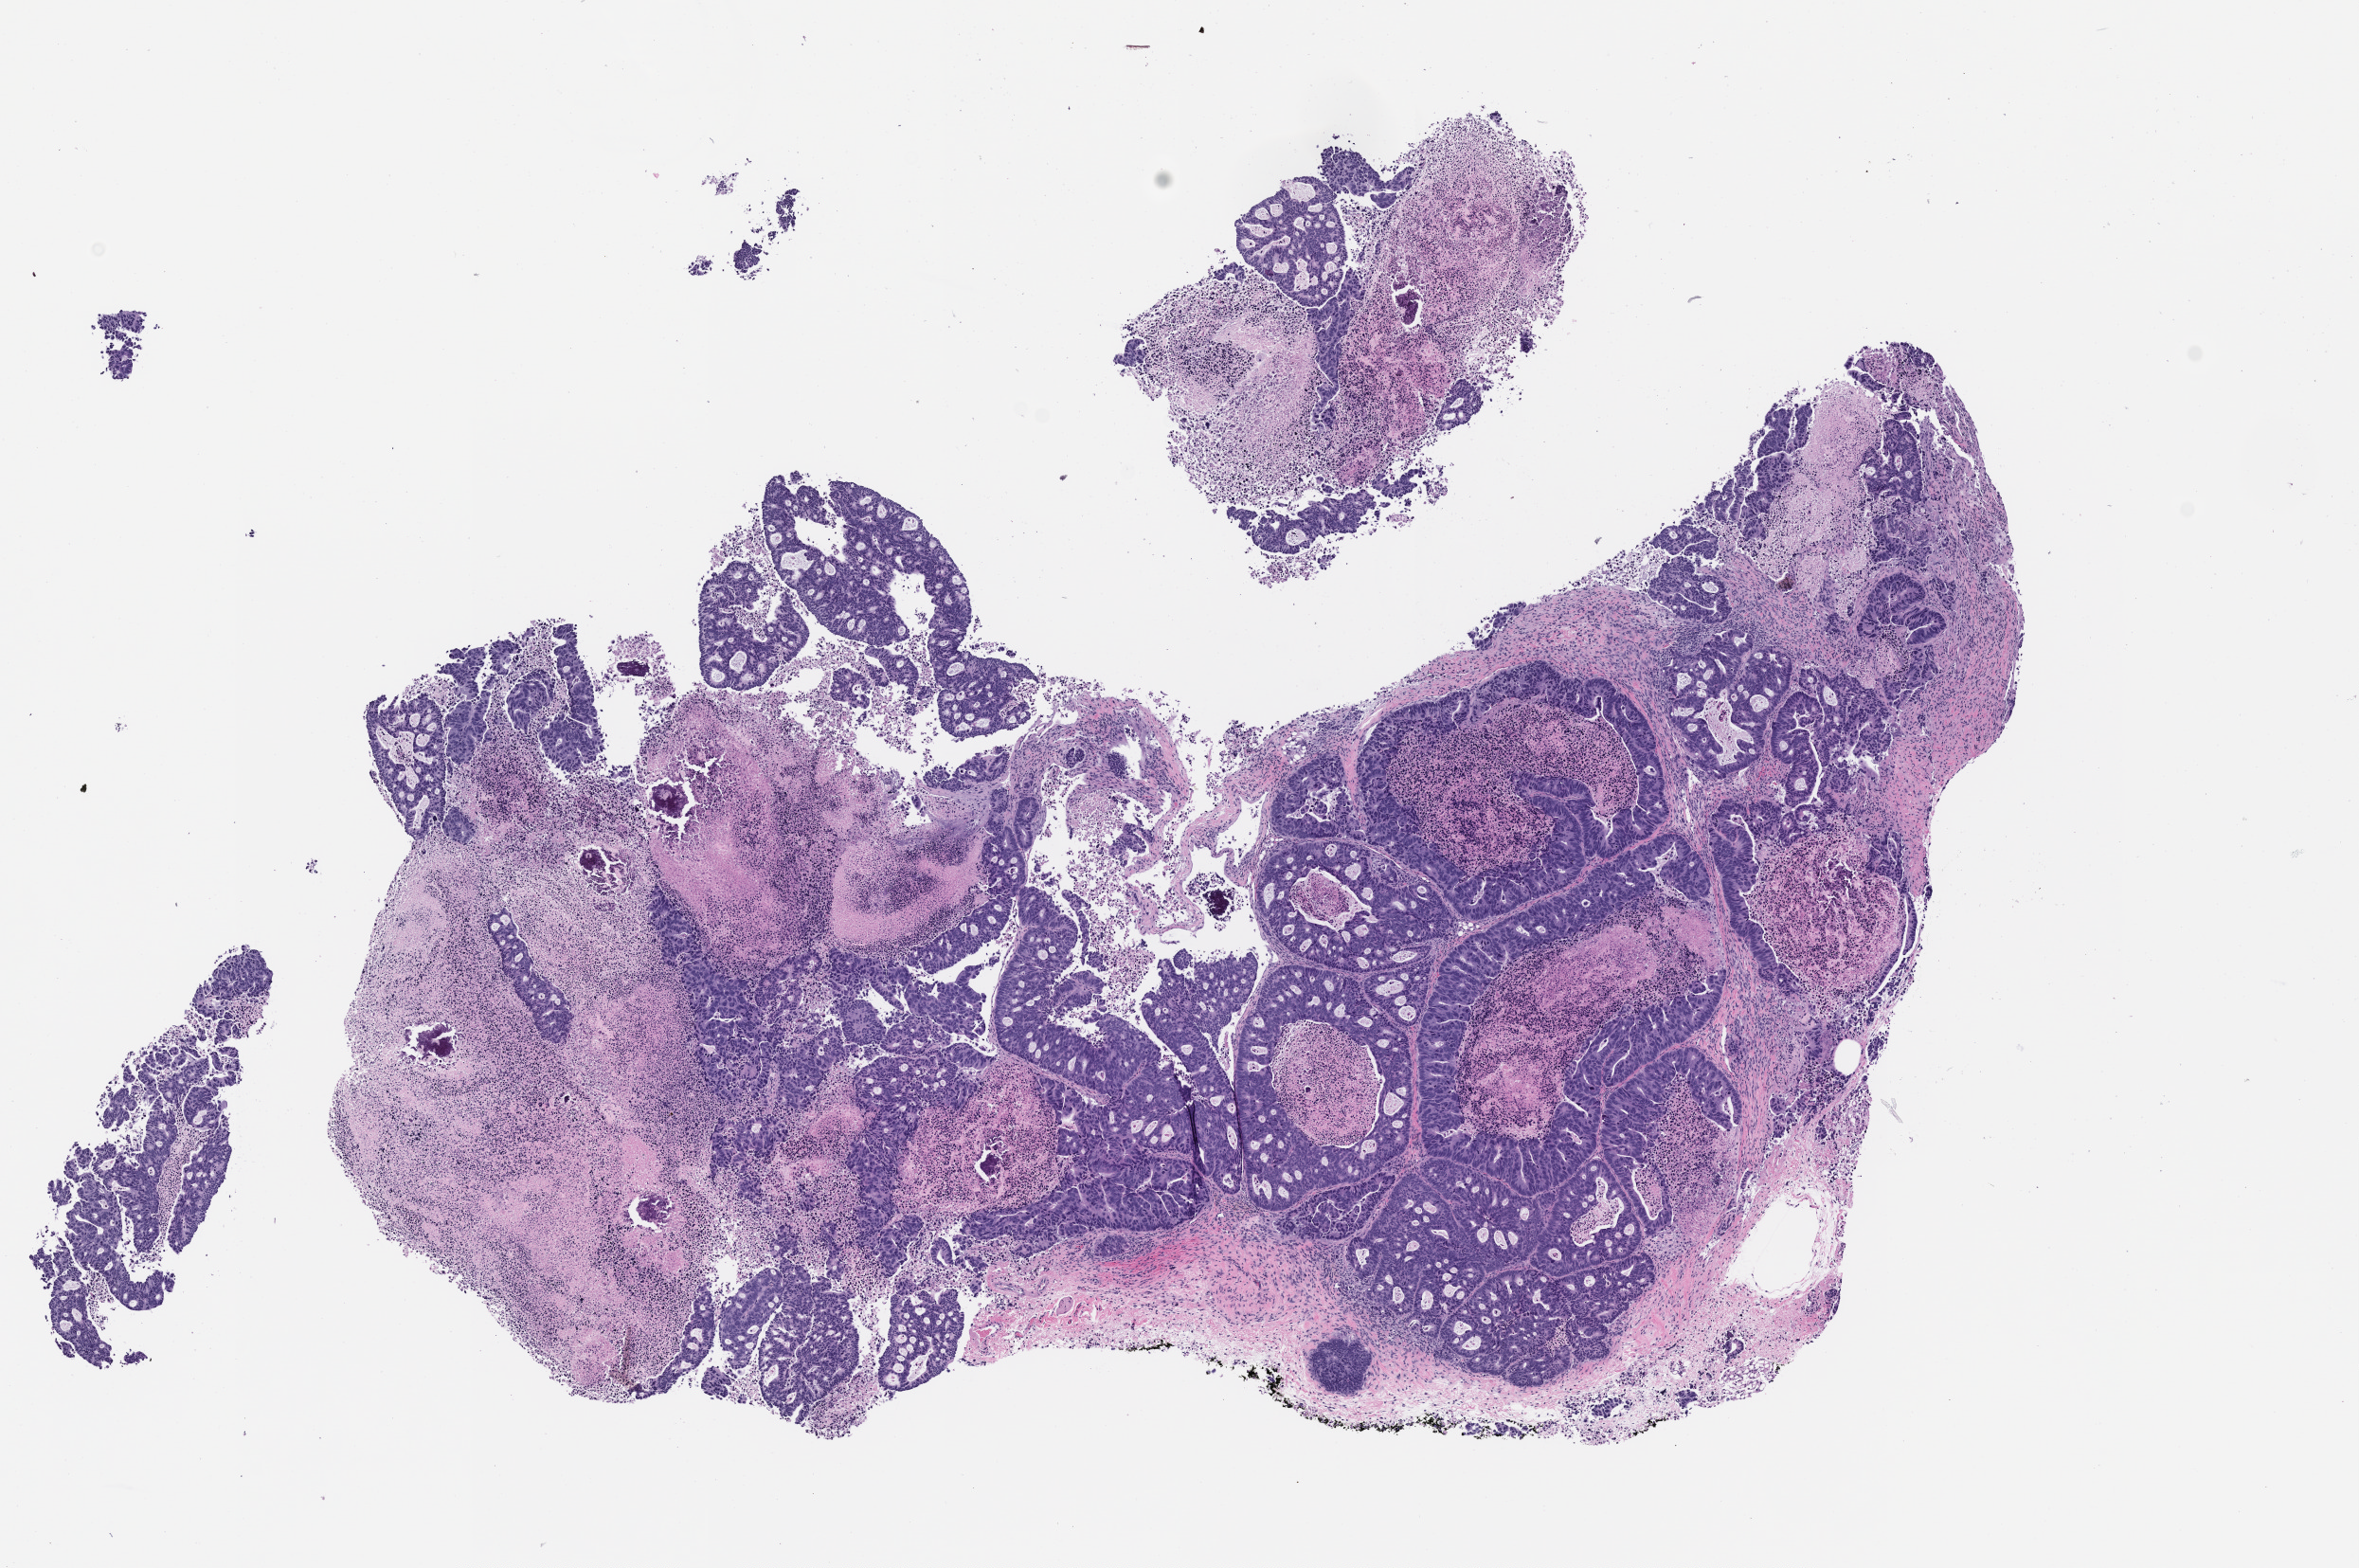
Haematoxylin and eosin whole-slide image of a patient-derived xenograft (PDX) tumor grown in a mouse, passage 2, shown as a low-resolution overview of the whole scanned area (about 10.0 x 6.7 mm); FFPE section; originating tumor site category: rectum.
Originating patient diagnosis: Rectal Adenocarcinoma.